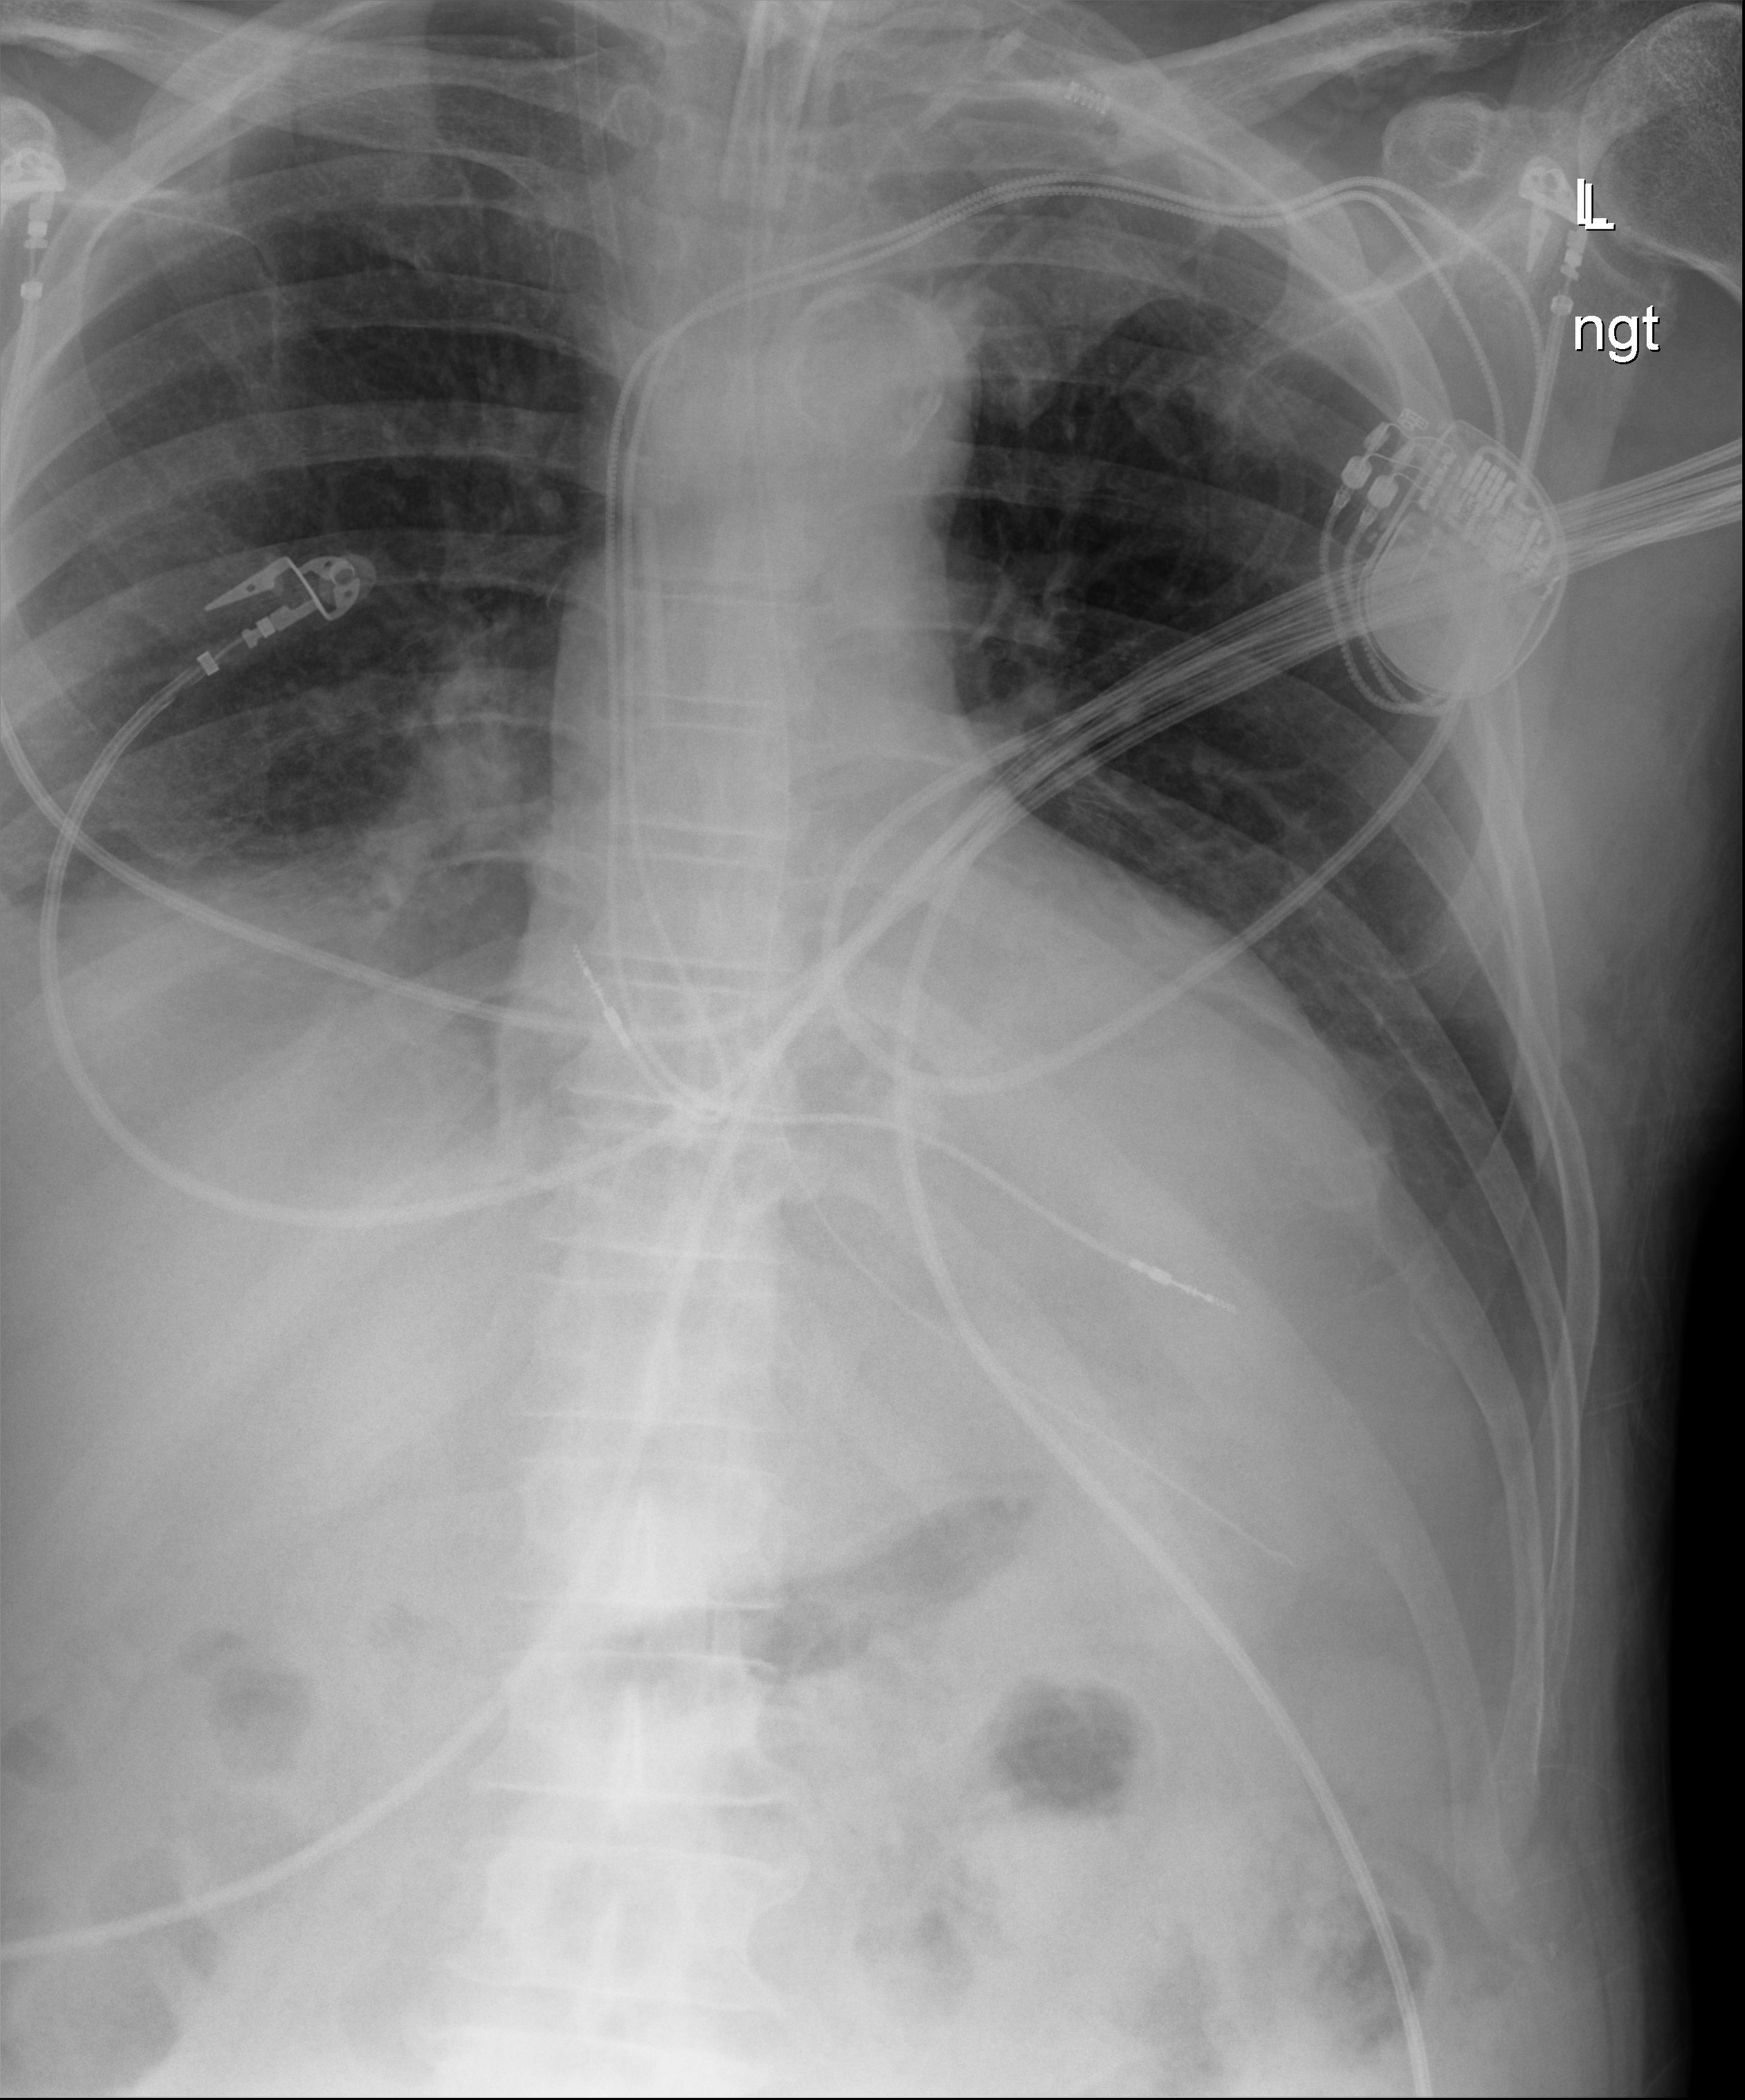
Chest radiograph, anteroposterior (AP) projection. Male patient hospitalised with COVID-19, age 60–74 years.
From the hospital-stay record, not from the radiograph (when in the stay this image was taken is not recorded): mechanically ventilated during this hospital stay: yes.